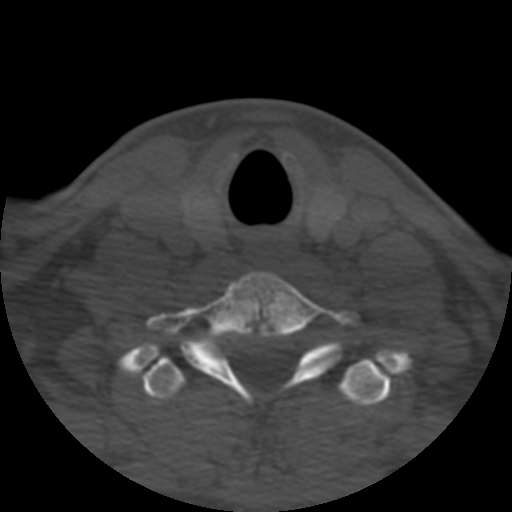
CT including the spine, one axial slice; position 459 of 508 along the scan axis; 120 kVp; bone window (W 1800 / L 400 HU); 1.25 mm slice thickness; 512 × 512 image matrix, field of view 160 × 160 mm. Patient age 57 years. Case-level facts recorded for this patient, not image findings: primary cancer: prostate.
Outlined on this slice (semi-automatically segmented with operator editing):
- T1 vertebra: bounding box <142,357,391,406> (left, top, right, bottom; pixels)